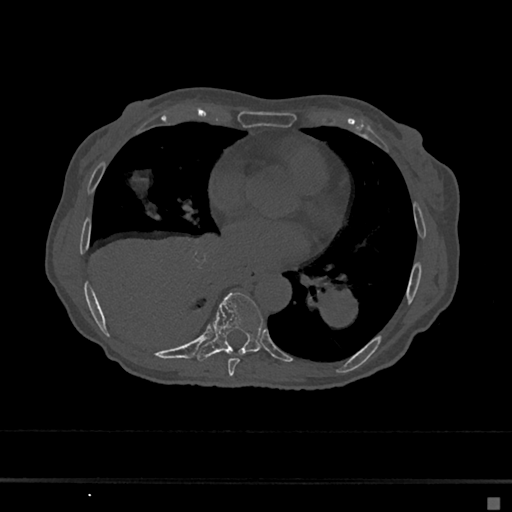
CT including the spine, one axial slice; slice 340 of 797 in the series (ordered by position); bone window (W 1800 / L 400 HU); 0.5 mm slice thickness; 512 × 512 image matrix. Patient: female, 68 years. Case-level facts recorded for this patient, not image findings: primary cancer: renal.
Structures marked on this image (semi-automatic segmentation, software-assisted and operator-edited):
- T7 vertebra: bounding box <228,358,240,377> (left, top, right, bottom; pixels)
- T8 vertebra: <197,292,263,361>